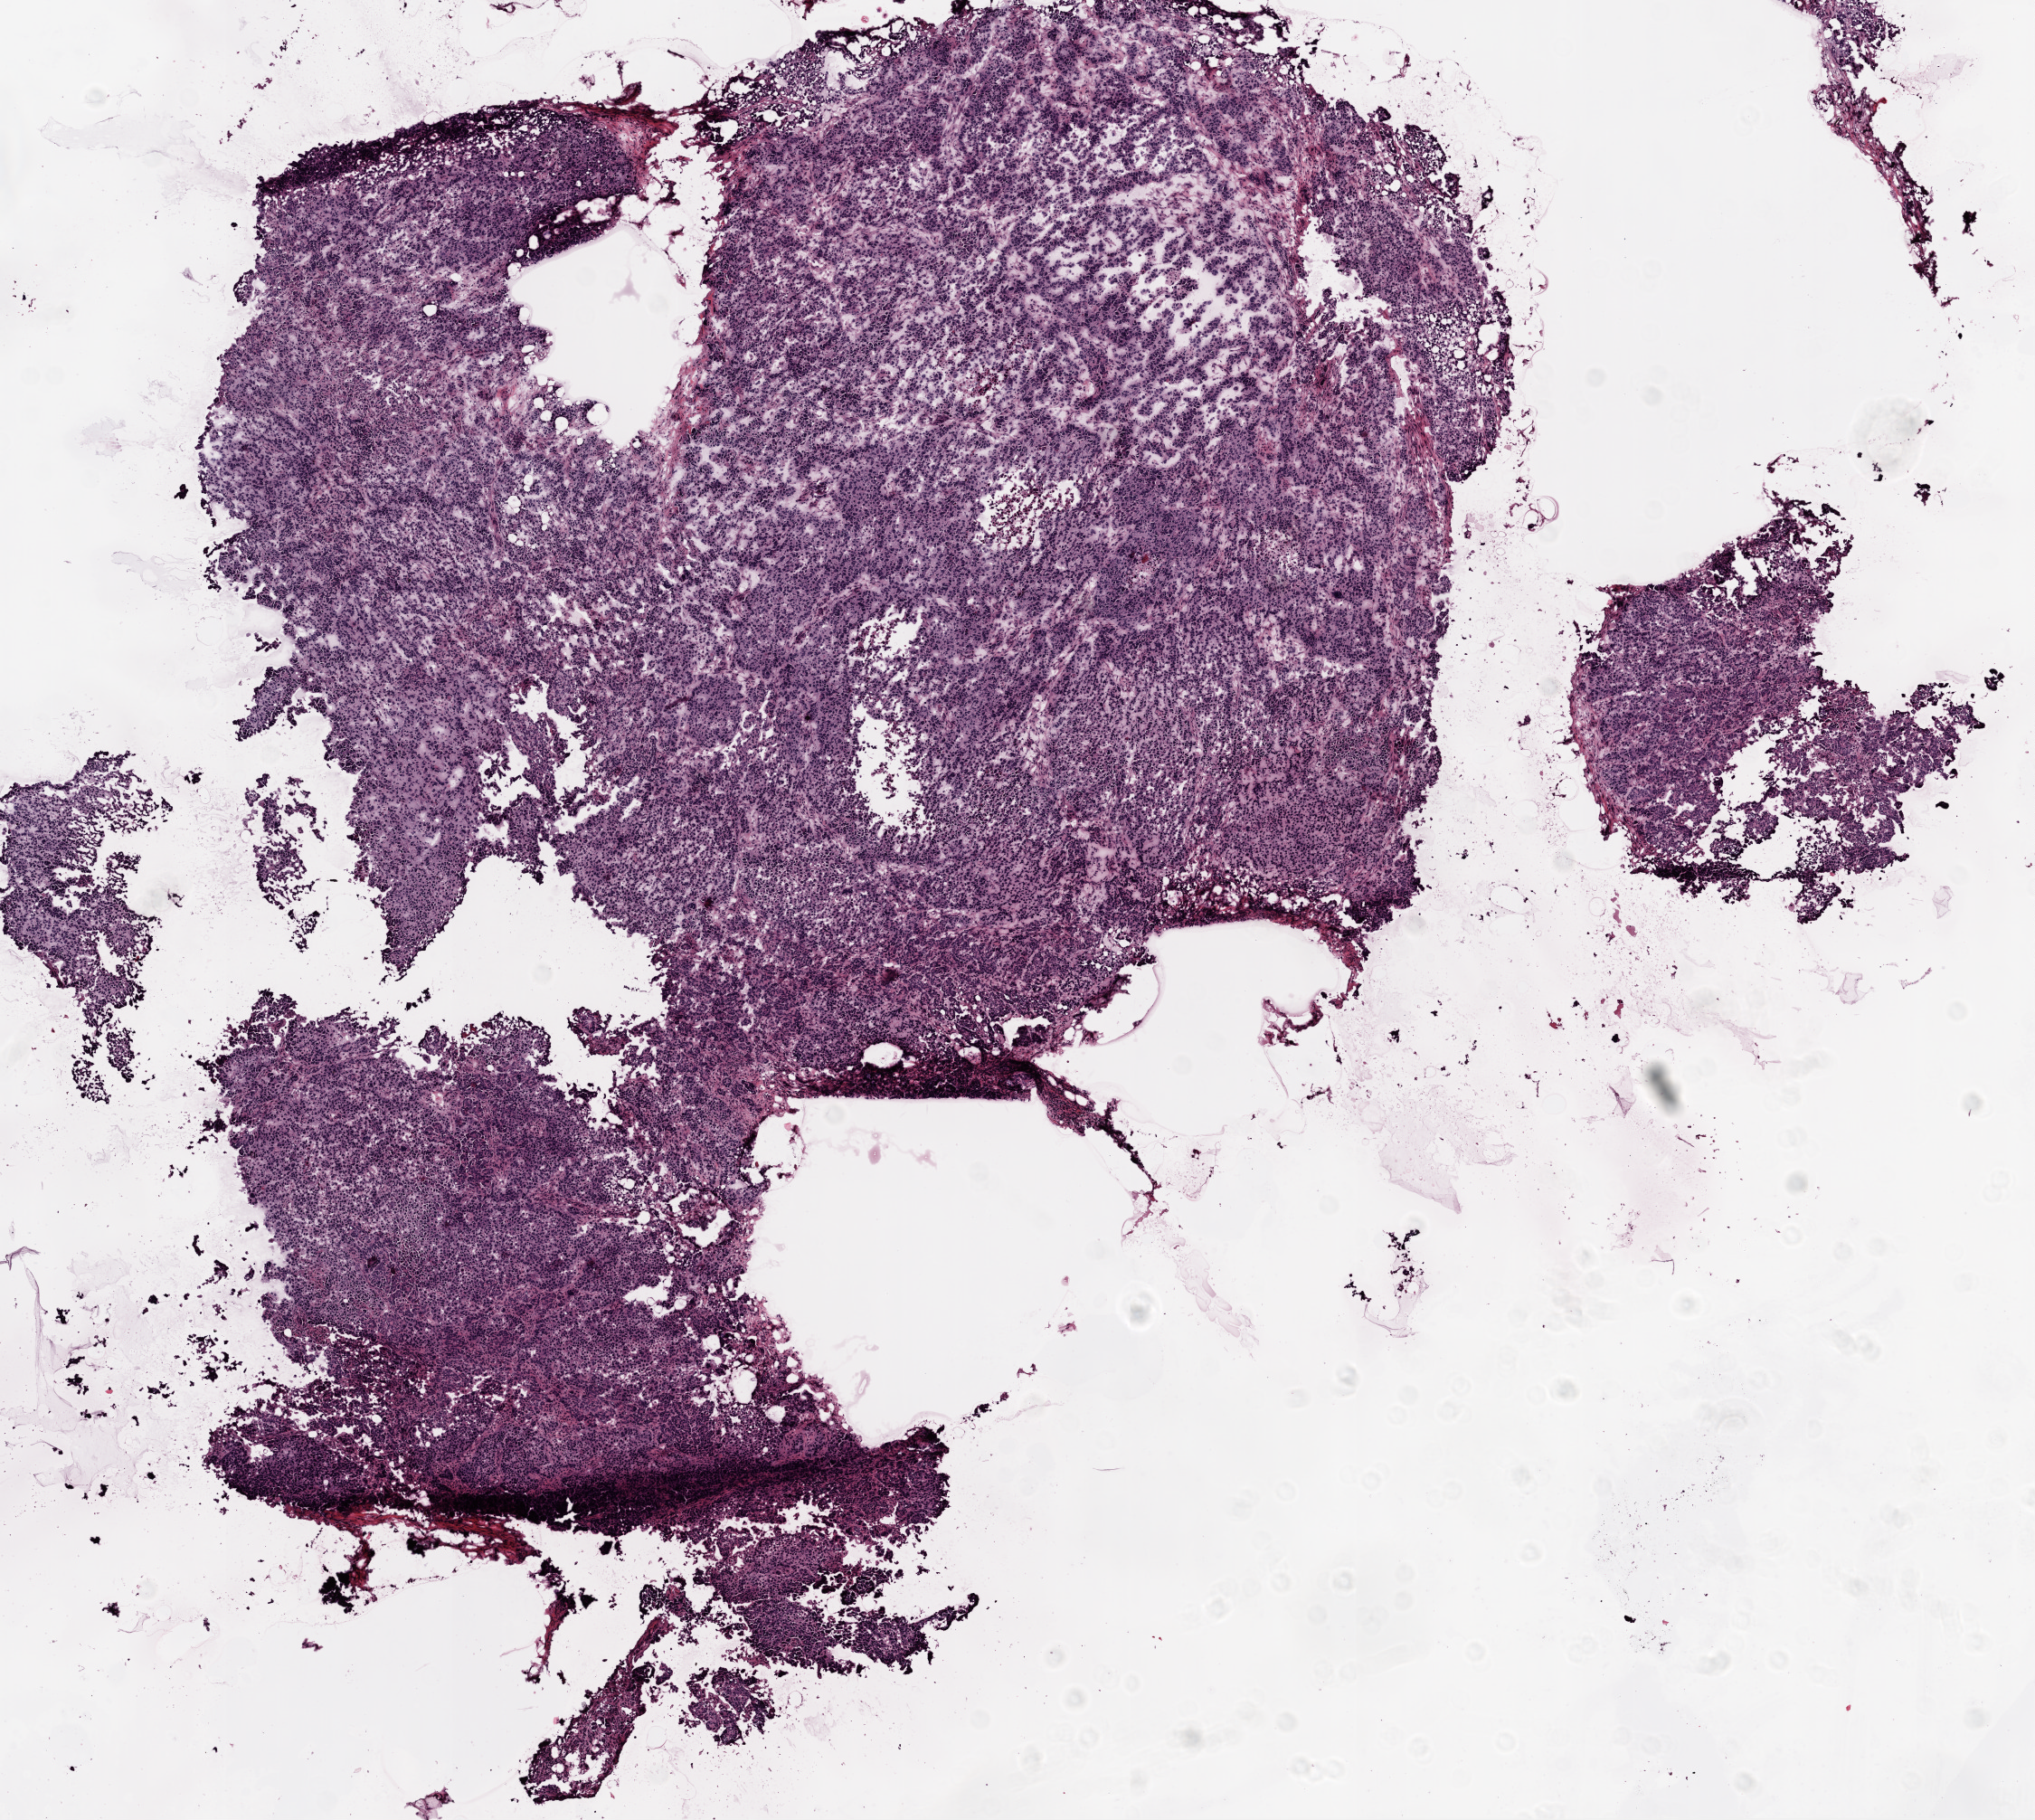
Digitized H&E tissue section (whole slide), a low-resolution overview of the entire scanned area, about 9.0 x 8.1 mm (from a 20x scan), frozen section from the top of the tissue portion, primary tumour sample from the ovary. Female patient; age at initial diagnosis 56 years. Pathologist review of this section (percent, as recorded): tumour cells 98%, tumour nuclei 90%.
Diagnosis: Serous cystadenocarcinoma, NOS.